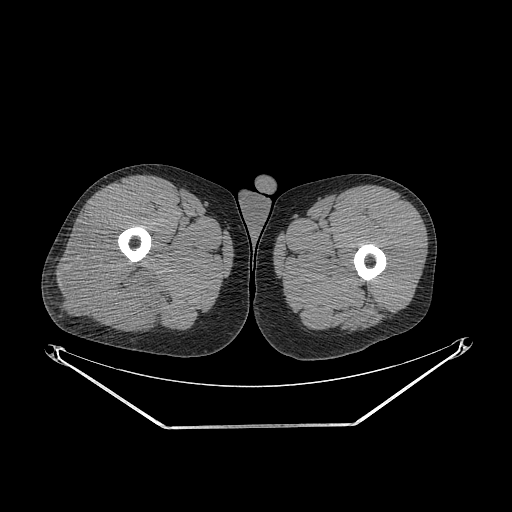
CT of an extremity soft-tissue mass (from a PET/CT study), one axial slice. Position 257 of 267 along the scan axis. Reconstruction kernel STANDARD. Soft-tissue window (W 400 / L 40 HU). 3.75 mm slice thickness. 512 × 512 image matrix. Male patient. Case-level facts recorded for this patient, not image findings: histological type: poorly differentiated synovial sarcoma; grade: high; site of the primary tumour: right buttock.
Structures marked on this image (expert contour drawn on MRI and transferred to this co-registered scan by the dataset authors):
- gross tumour volume including surrounding oedema: bounding box [x1, y1, x2, y2] px = [53, 217, 161, 330]
- gross tumour volume (mass): [53, 217, 161, 330]